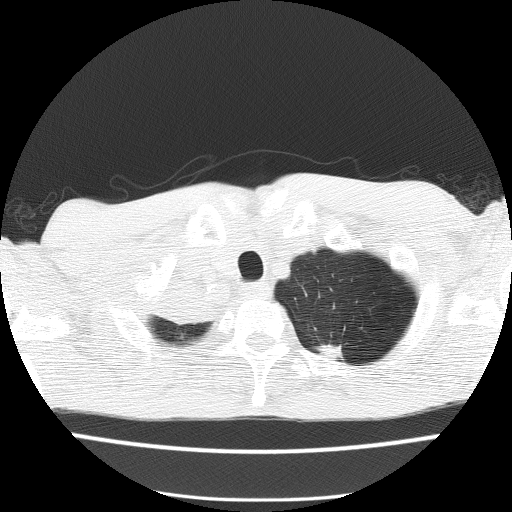
Low-dose screening chest CT, one axial slice; slice 132 of 150 in the series (ordered by position); reconstruction kernel FC51; lung window (W 1500 / L -600 HU); 2 mm slice thickness; 512 × 512 image matrix, field of view 336 × 336 mm.
Structures marked on this image (outlined manually by an expert reader):
- lesion 1 (tumor, hilum of right lung): box from (x=159, y=284) to (x=214, y=323) px